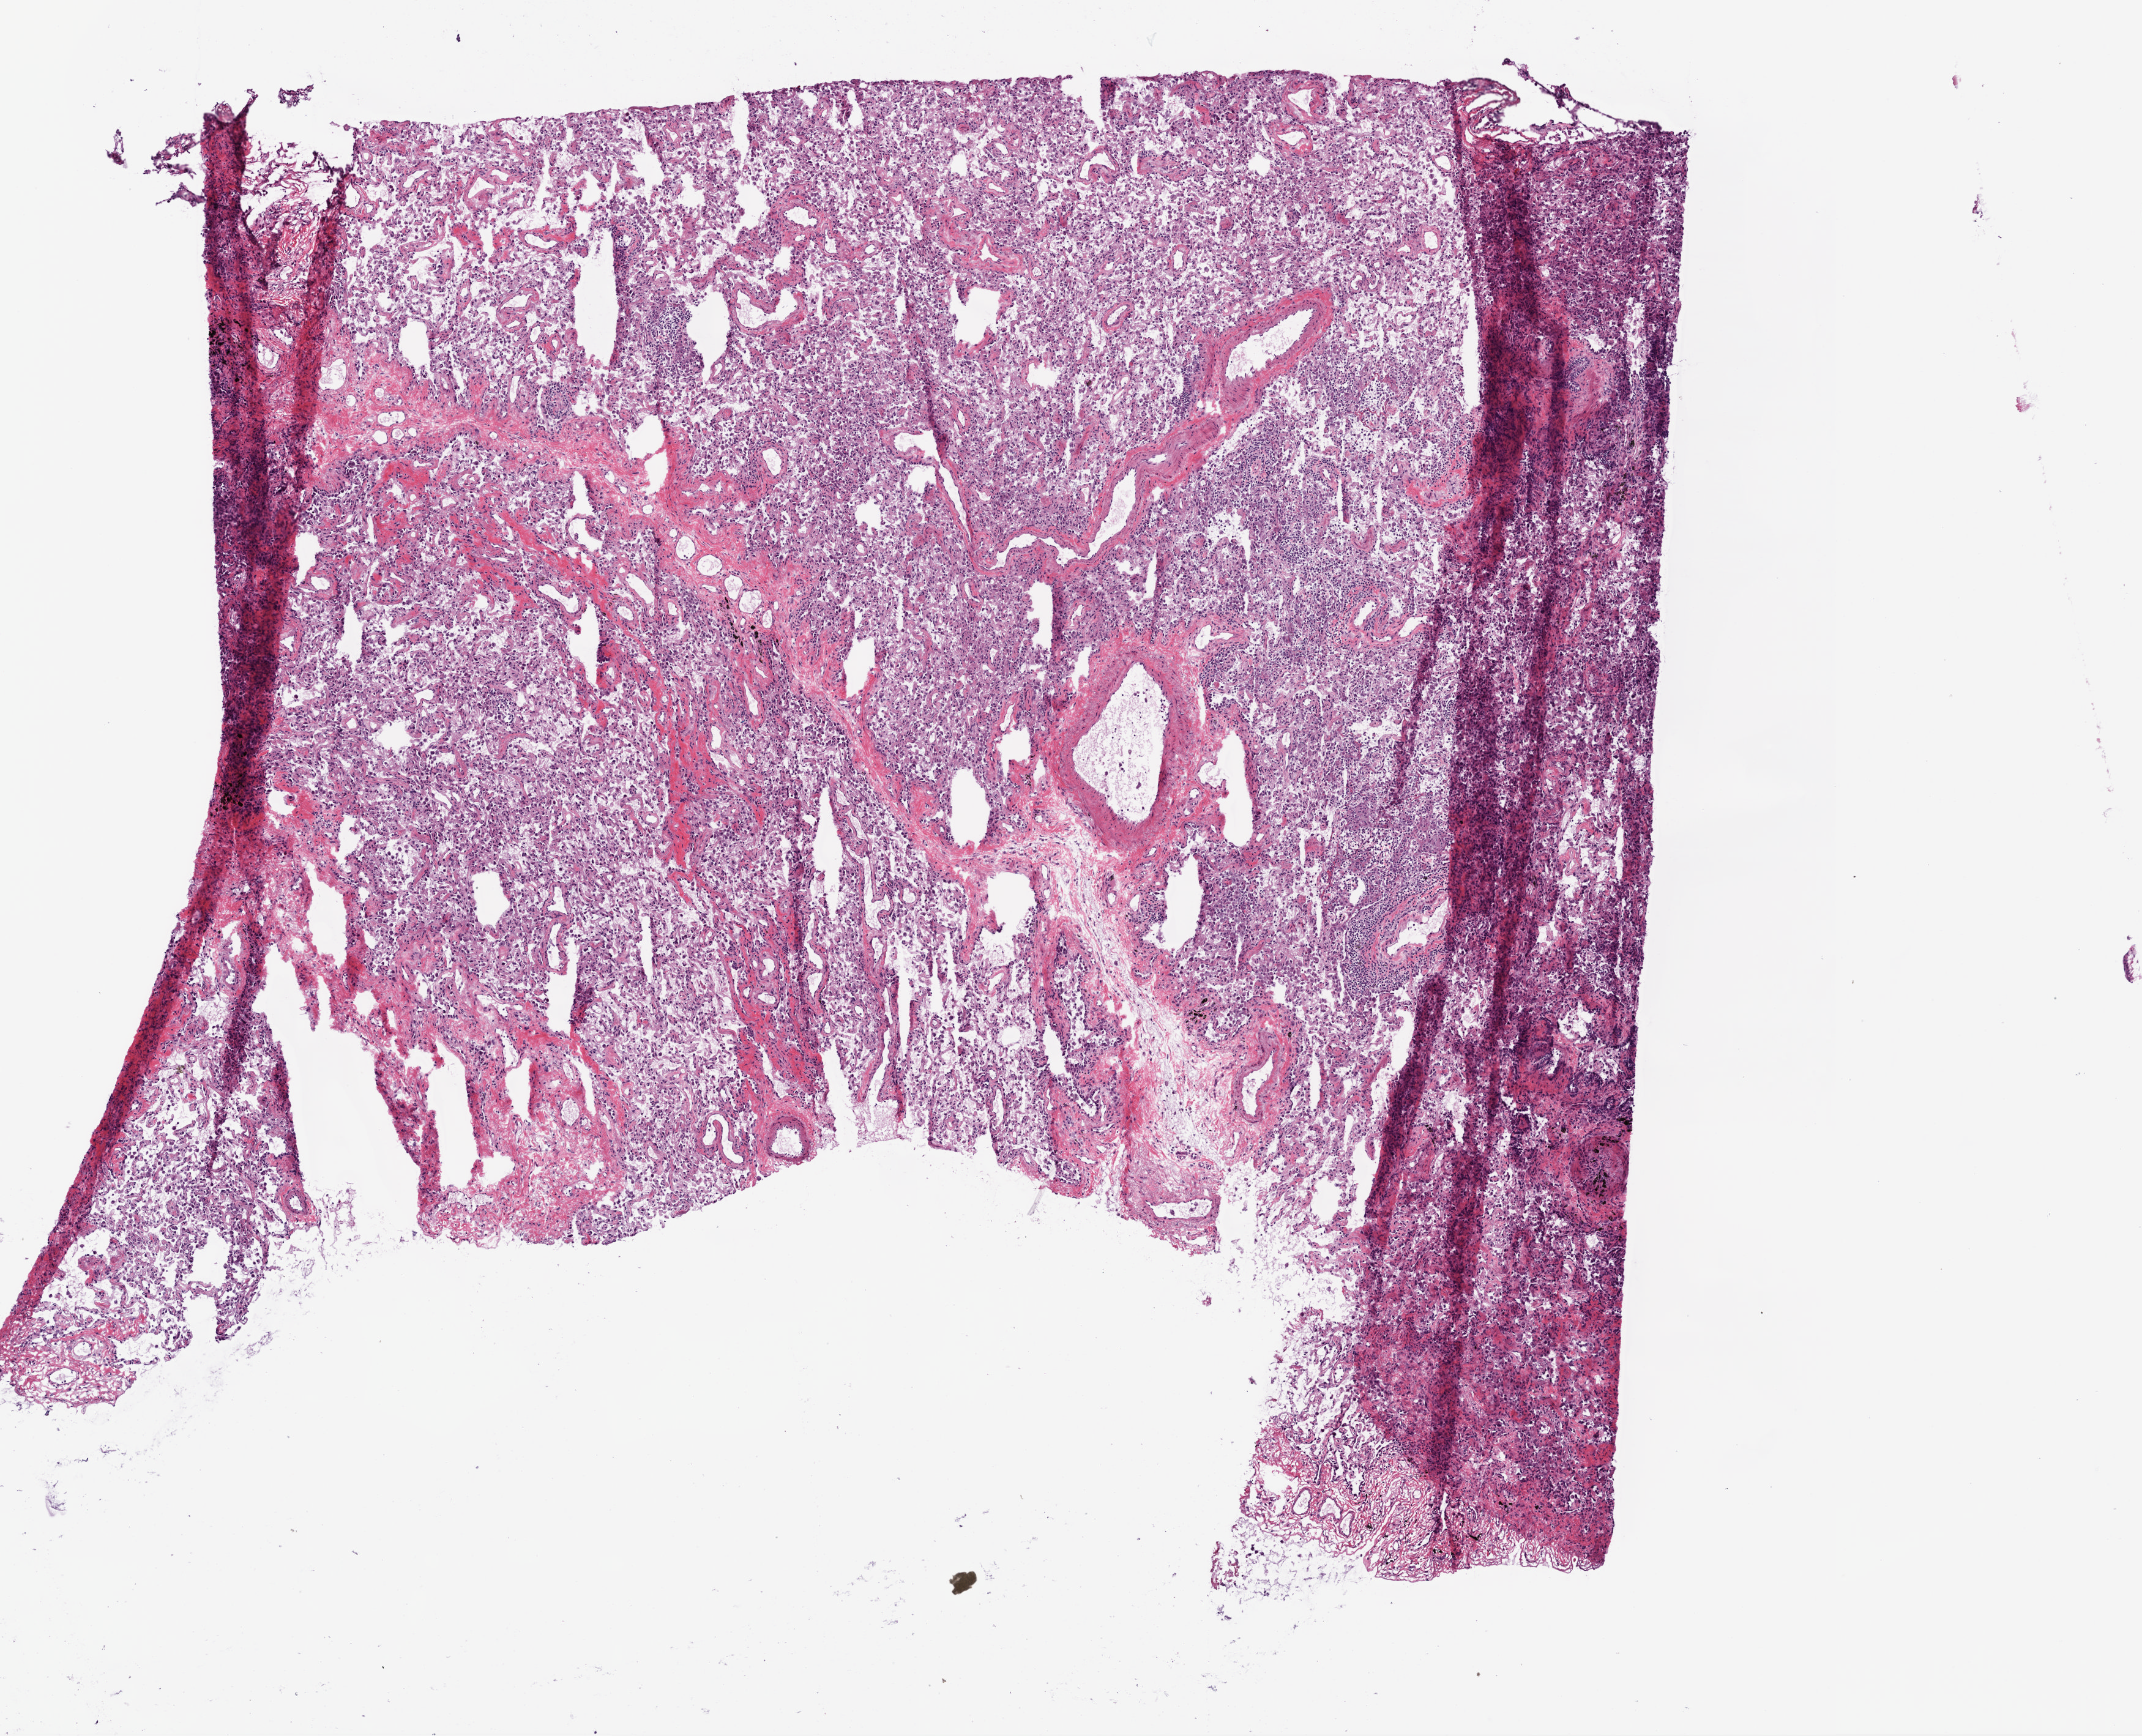
Digitized Hematoxylin and eosin (H&E) stained tissue section (whole slide), whole scanned area (about 7.0 x 5.7 mm) shown as a low-resolution overview, frozen section, lung, solid tissue normal (non-tumour tissue) sample. Patient: male, age at initial diagnosis 65 years.
This section: solid tissue normal sample (biorepository sample class). Patient diagnosis: Basaloid squamous cell carcinoma (upper lobe, lung).